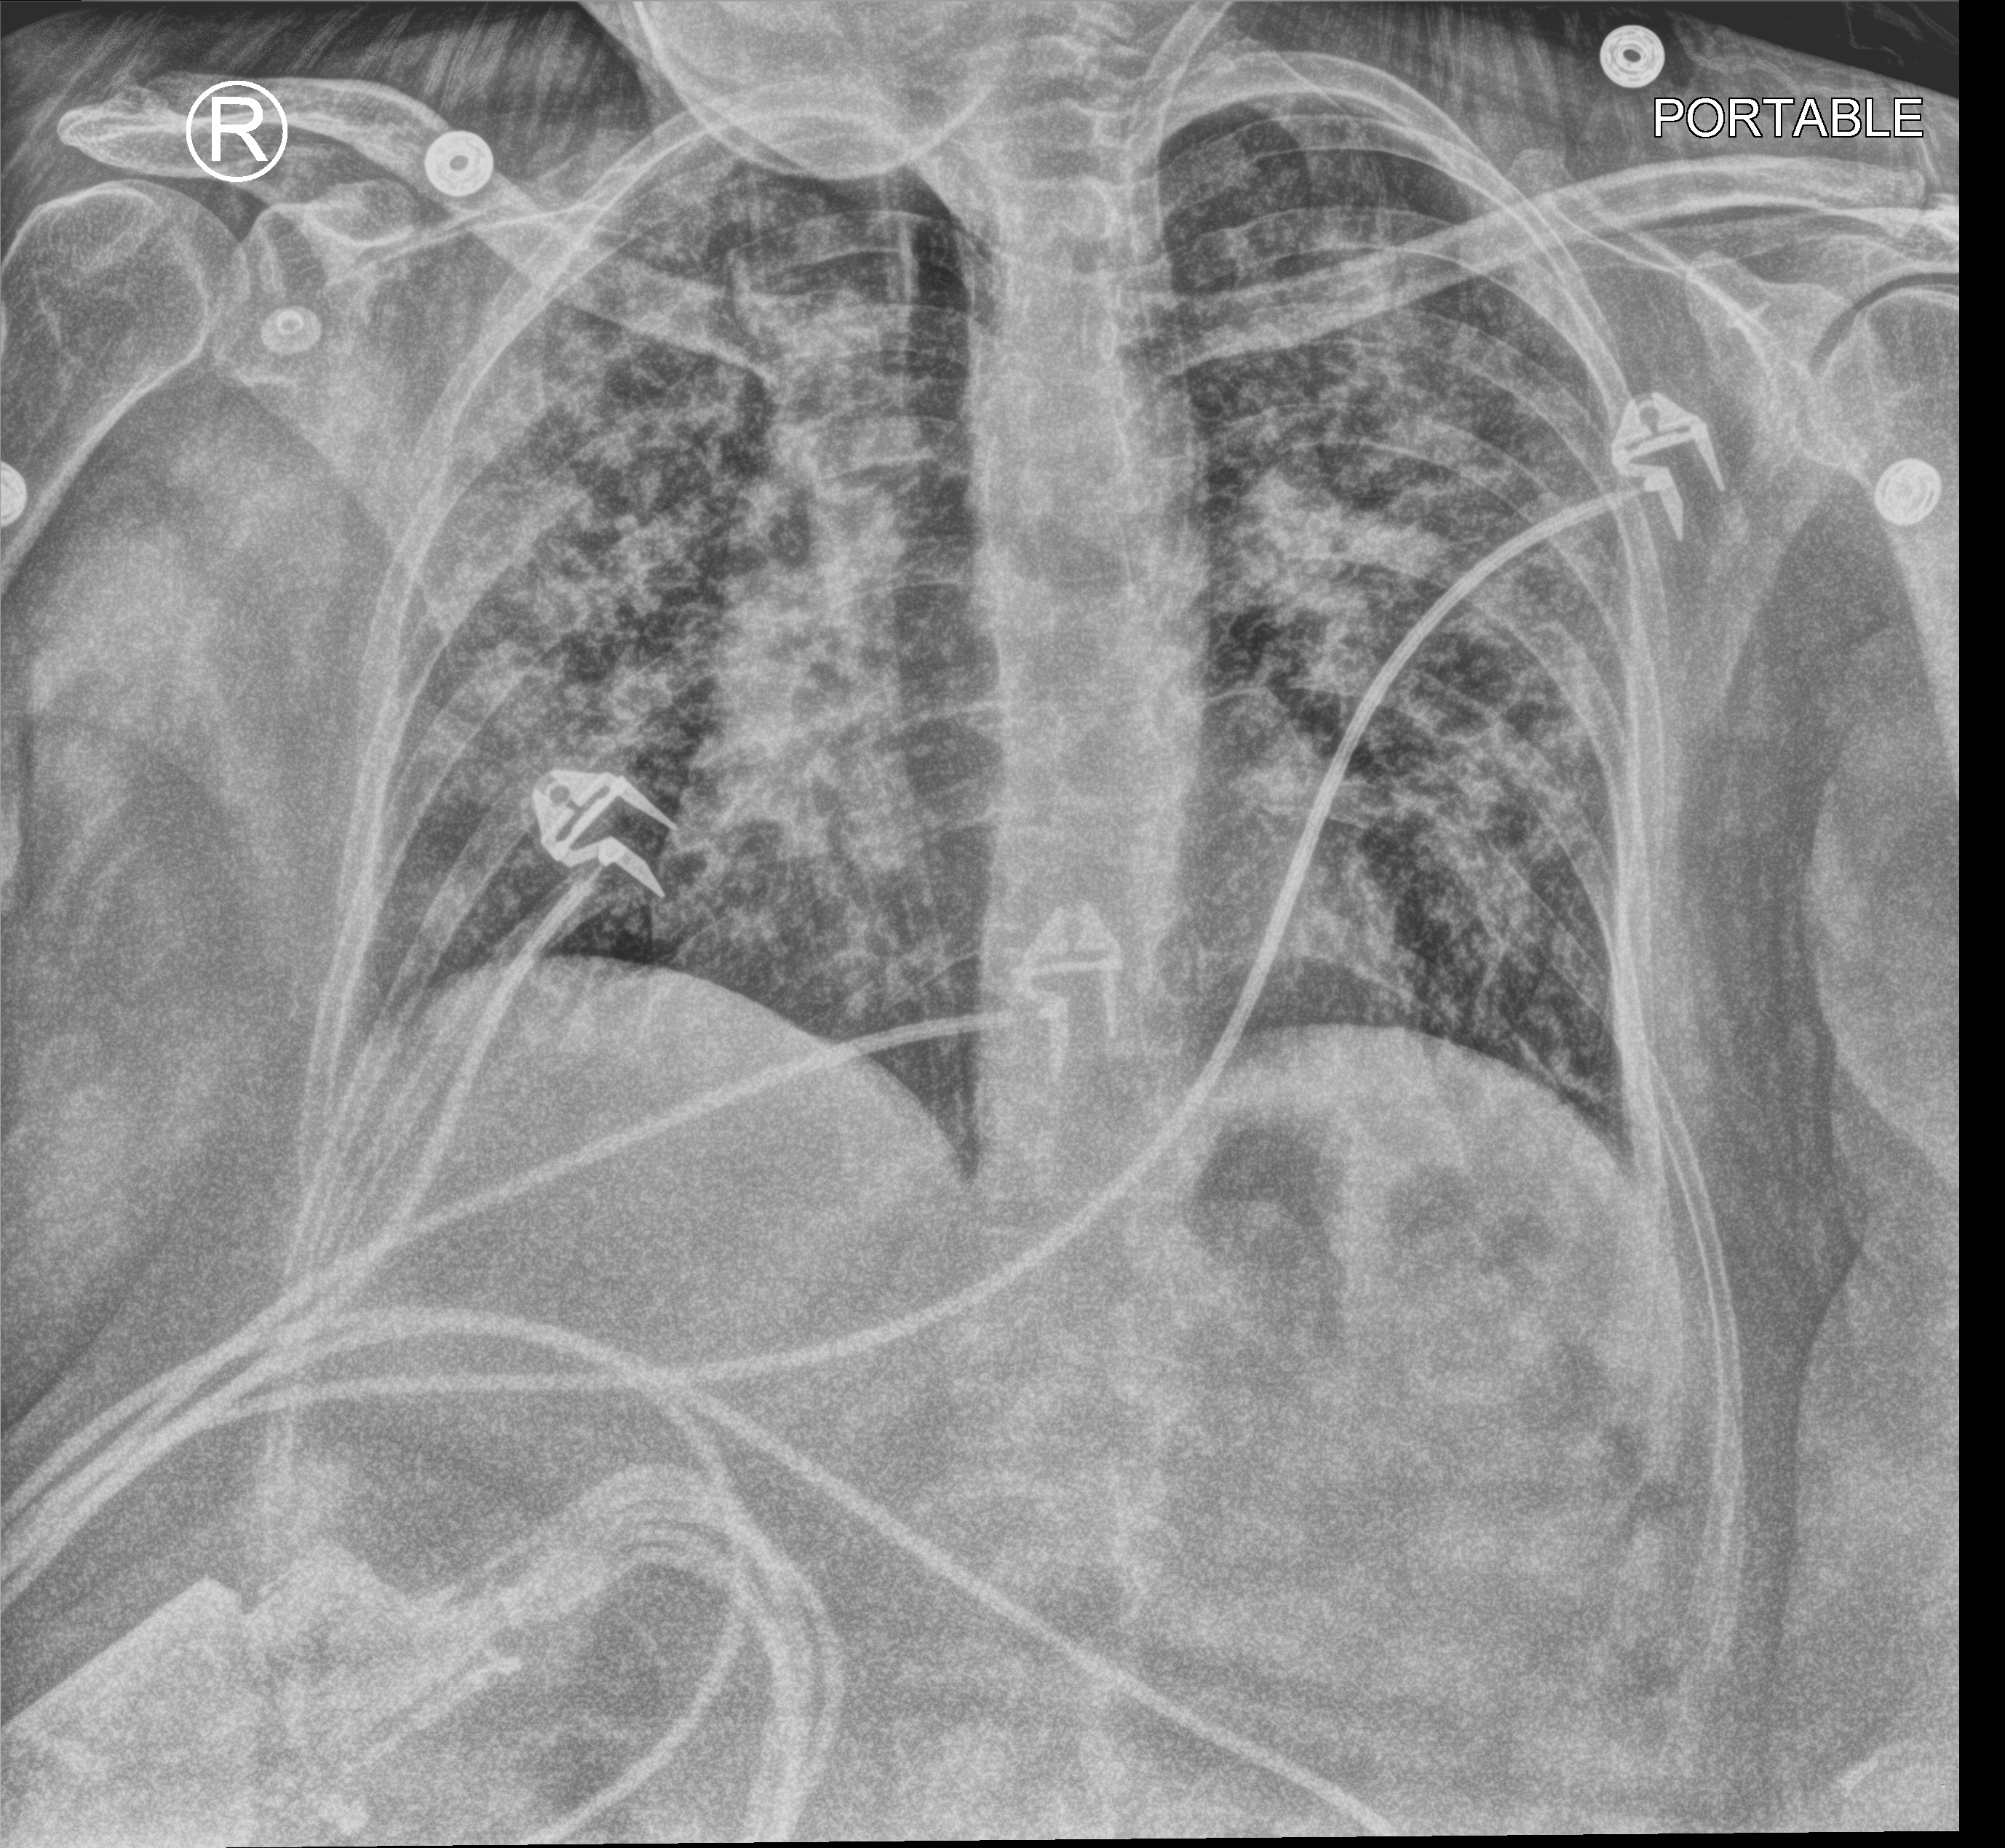
Portable chest radiograph; anteroposterior (AP) projection. Patient hospitalised with COVID-19; female, aged 18–59 years.
From the hospital-stay record, not from the radiograph (when in the stay this image was taken is not recorded):
- chronic kidney disease (admission record): no